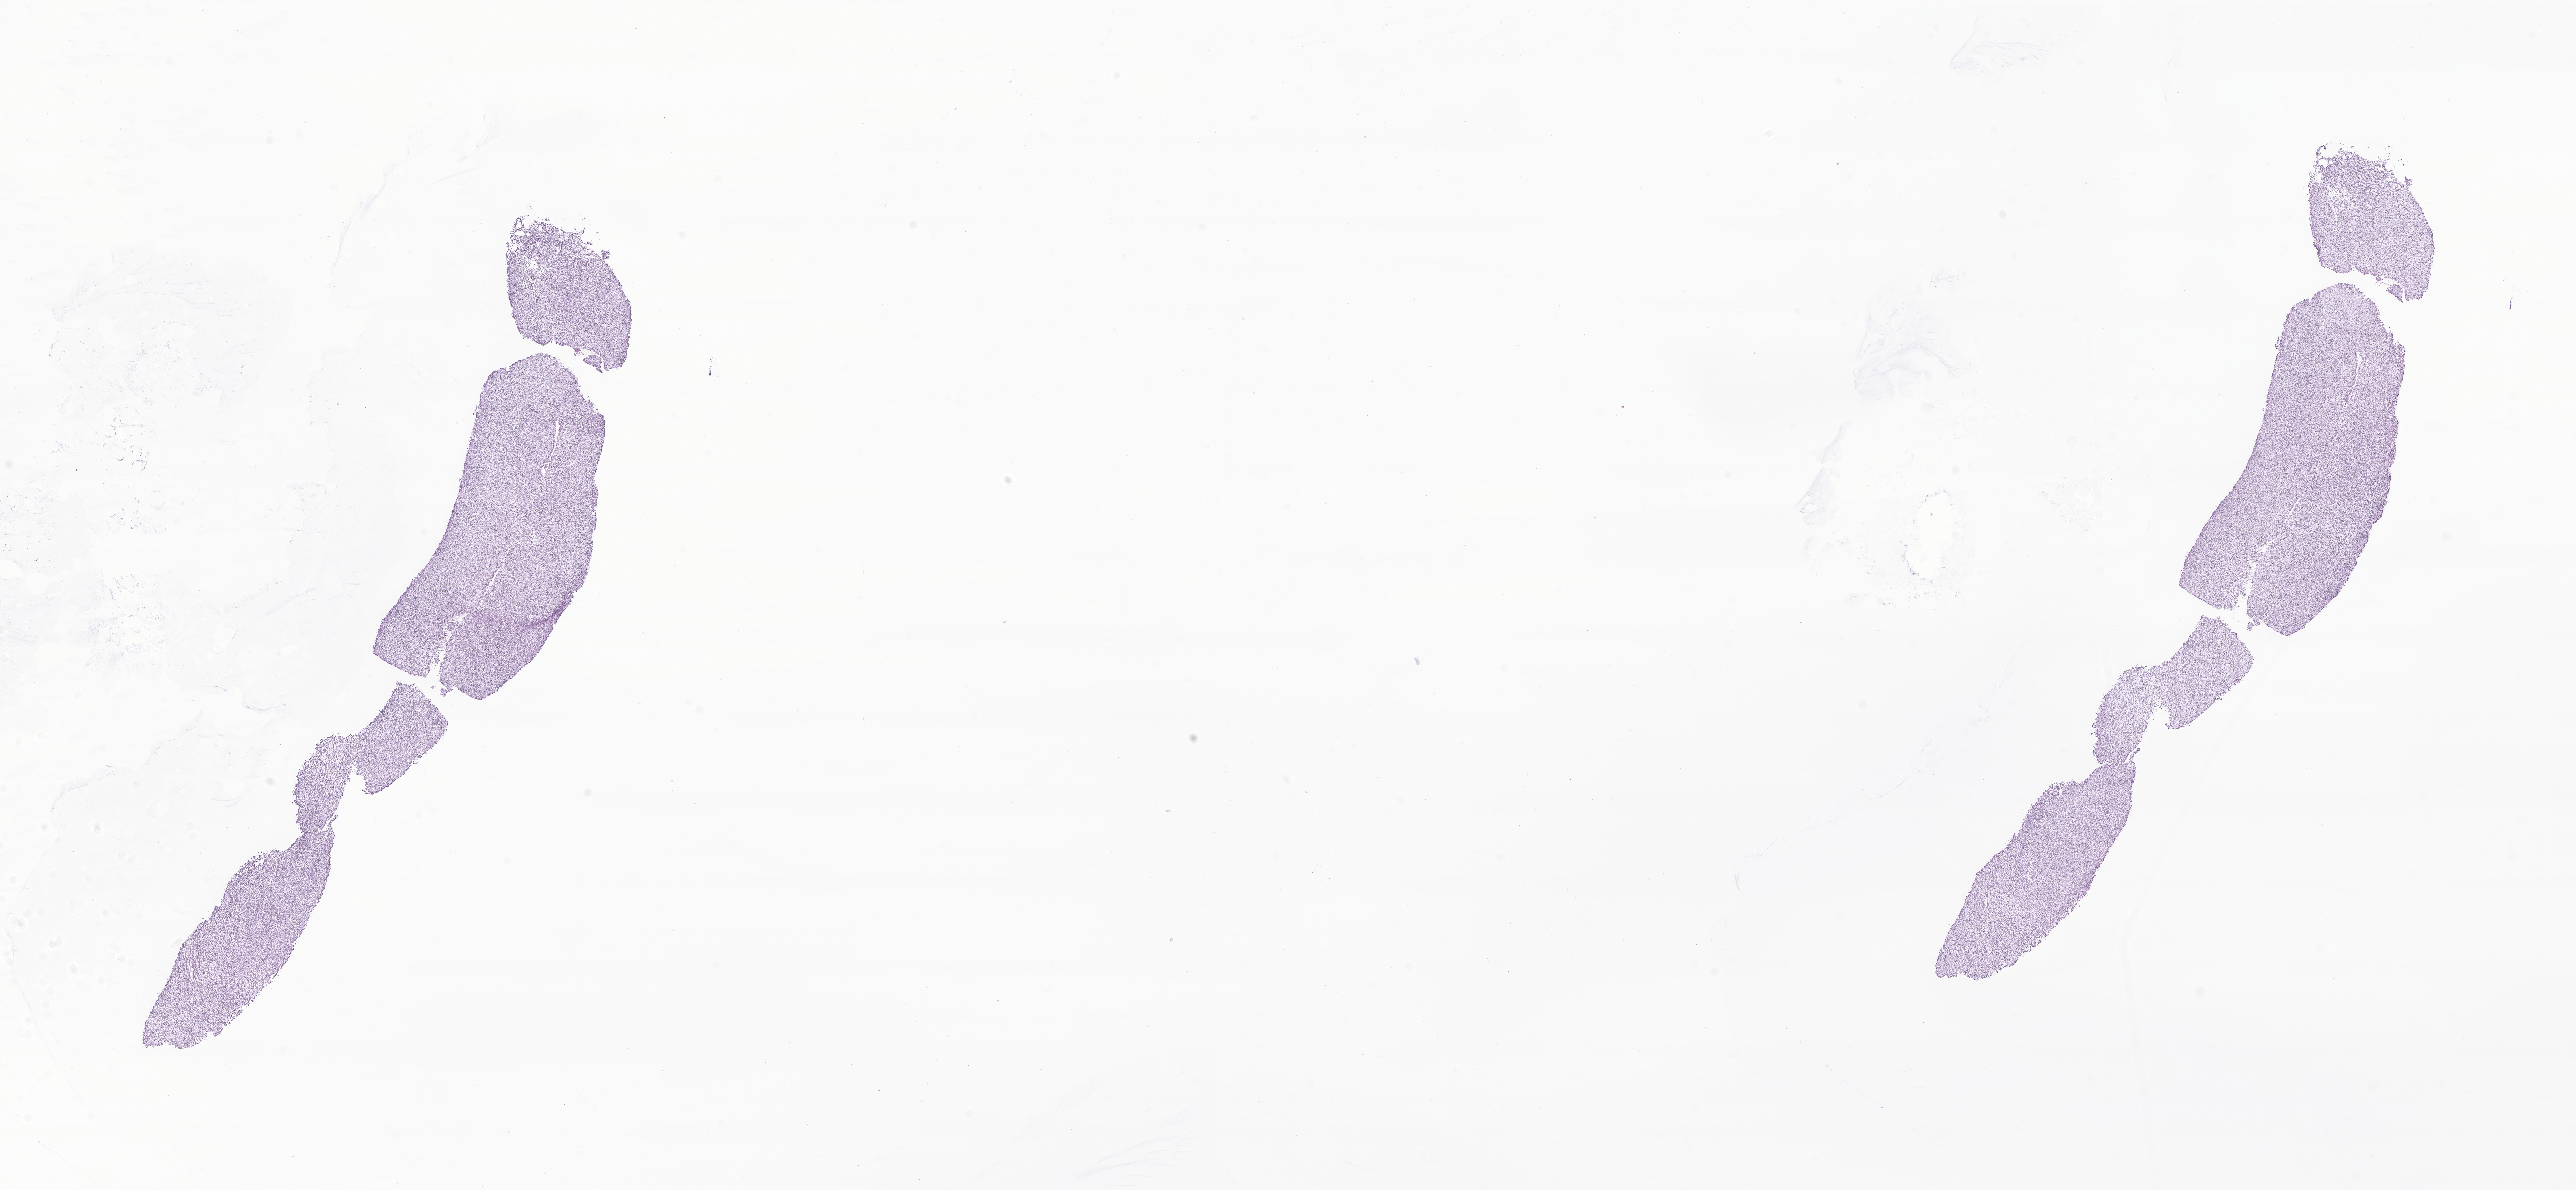
Whole-slide image, H&E stain of tumor tissue from the brain — shown as a low-resolution overview of the whole scanned area (about 33.4 x 15.4 mm); frozen section. Female patient, age 272 days.
Diagnosis: Neoplasm, uncertain whether benign or malignant.